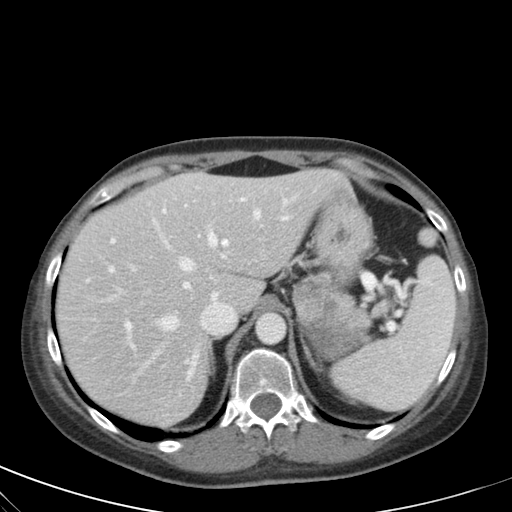
Contrast-enhanced abdominal CT, one axial slice. Slice 45 of 59 in the series (ordered by position). Intravenous contrast given. Soft-tissue window (W 400 / L 40 HU). 4 mm slice thickness. 512 × 512 image matrix. Female patient, age 28 years. Case-level facts recorded for this patient, not image findings: diagnosis: adrenocortical carcinoma; tumour side: left adrenal; tumour size at pathology: 7 cm.
Annotated regions visible in this slice (semi-automatic segmentation, software-assisted and operator-edited):
- mass: box from (x=293, y=273) to (x=372, y=360) px